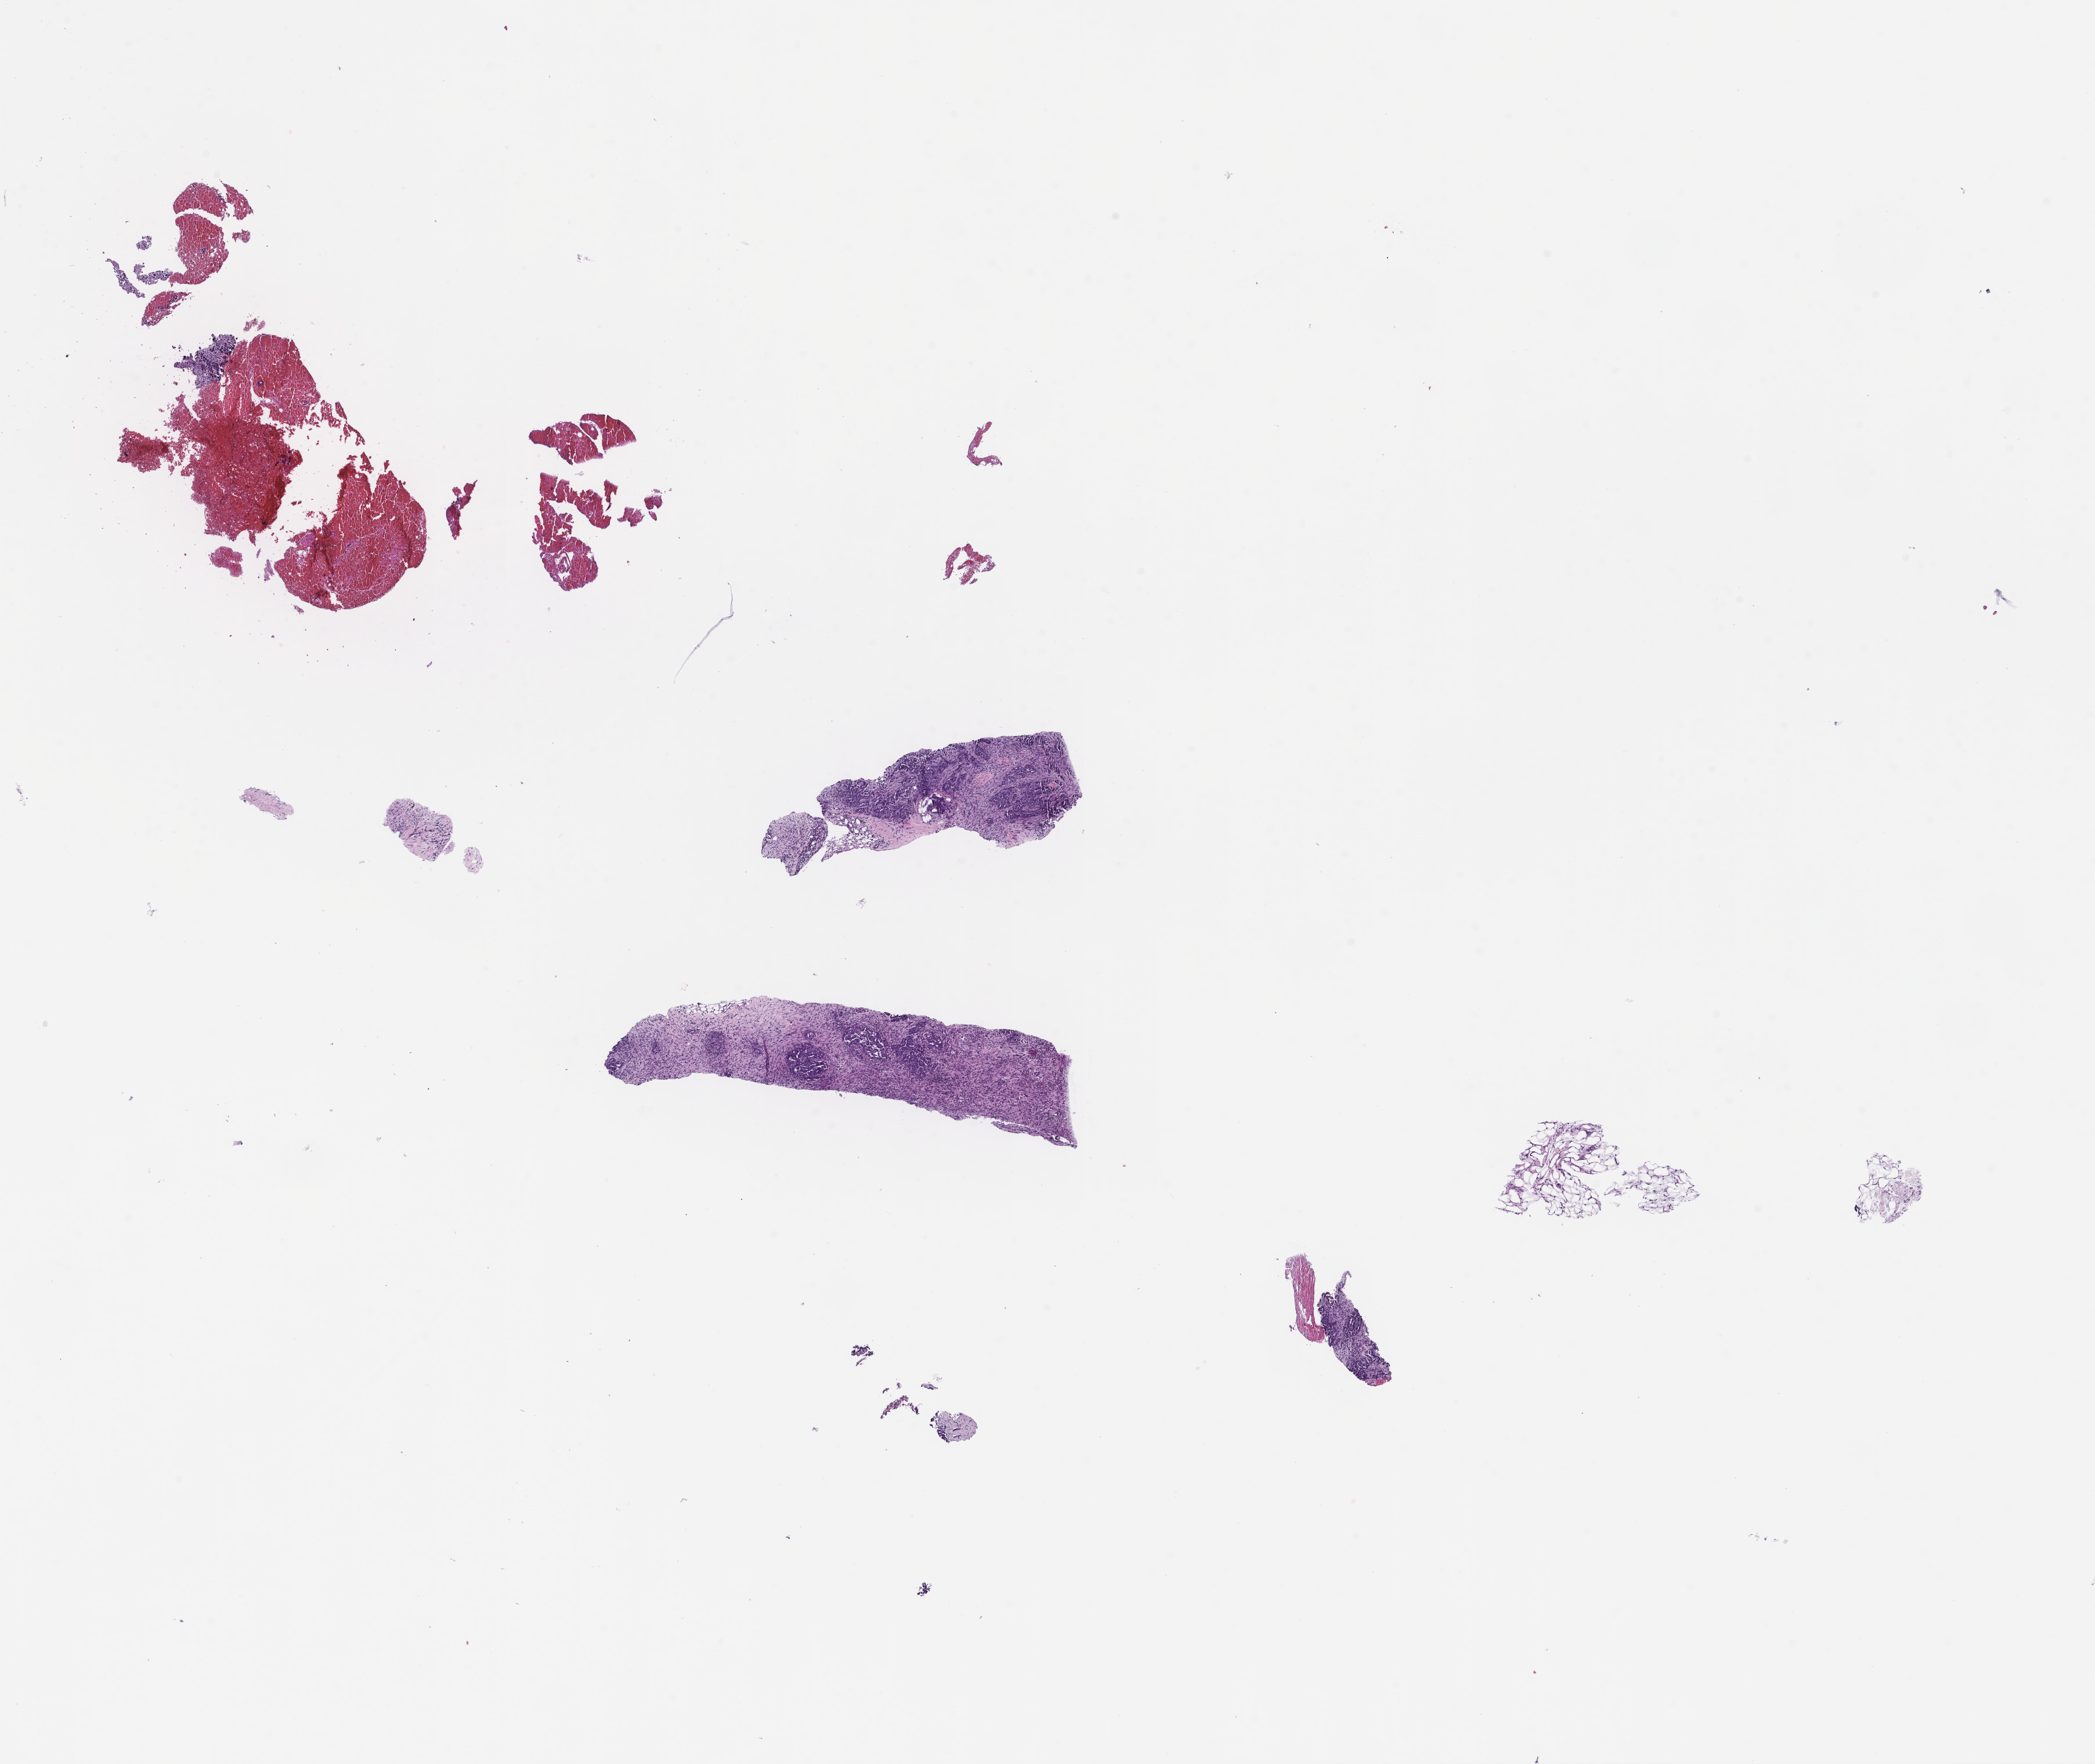
Whole-slide image, hematoxylin and eosin (H&E) stain — a low-resolution overview of the entire scanned area, about 14.6 x 12.3 mm; formalin-fixed paraffin-embedded section; archival tissue. Female patient.
This section: metastatic tumor tissue. Primary diagnosis of the patient: Ovarian Carcinoma.